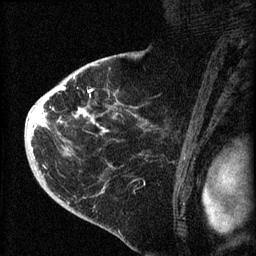
Breast MRI (dynamic contrast-enhanced), one sagittal slice; slice 46 of 60 in the series (ordered by position); dynamic contrast-enhanced series, image 2 of 4 at this slice position (ordered by acquisition); 1.5 T; TE 4.2 ms, TR 8.2 ms; 256 × 256 image matrix, field of view 180 × 180 mm. Patient: female, 71 years.
Structures marked on this image (semi-automatic segmentation, software-assisted and operator-edited):
- analysis volume of interest (the breast-tissue region the enhancement analysis was run in; not a lesion): box from (x=35, y=75) to (x=148, y=190) px
- tumour enhancement mask (voxels above the 70 % enhancement threshold inside the analysis volume of interest): (x=35, y=77)–(x=109, y=132)